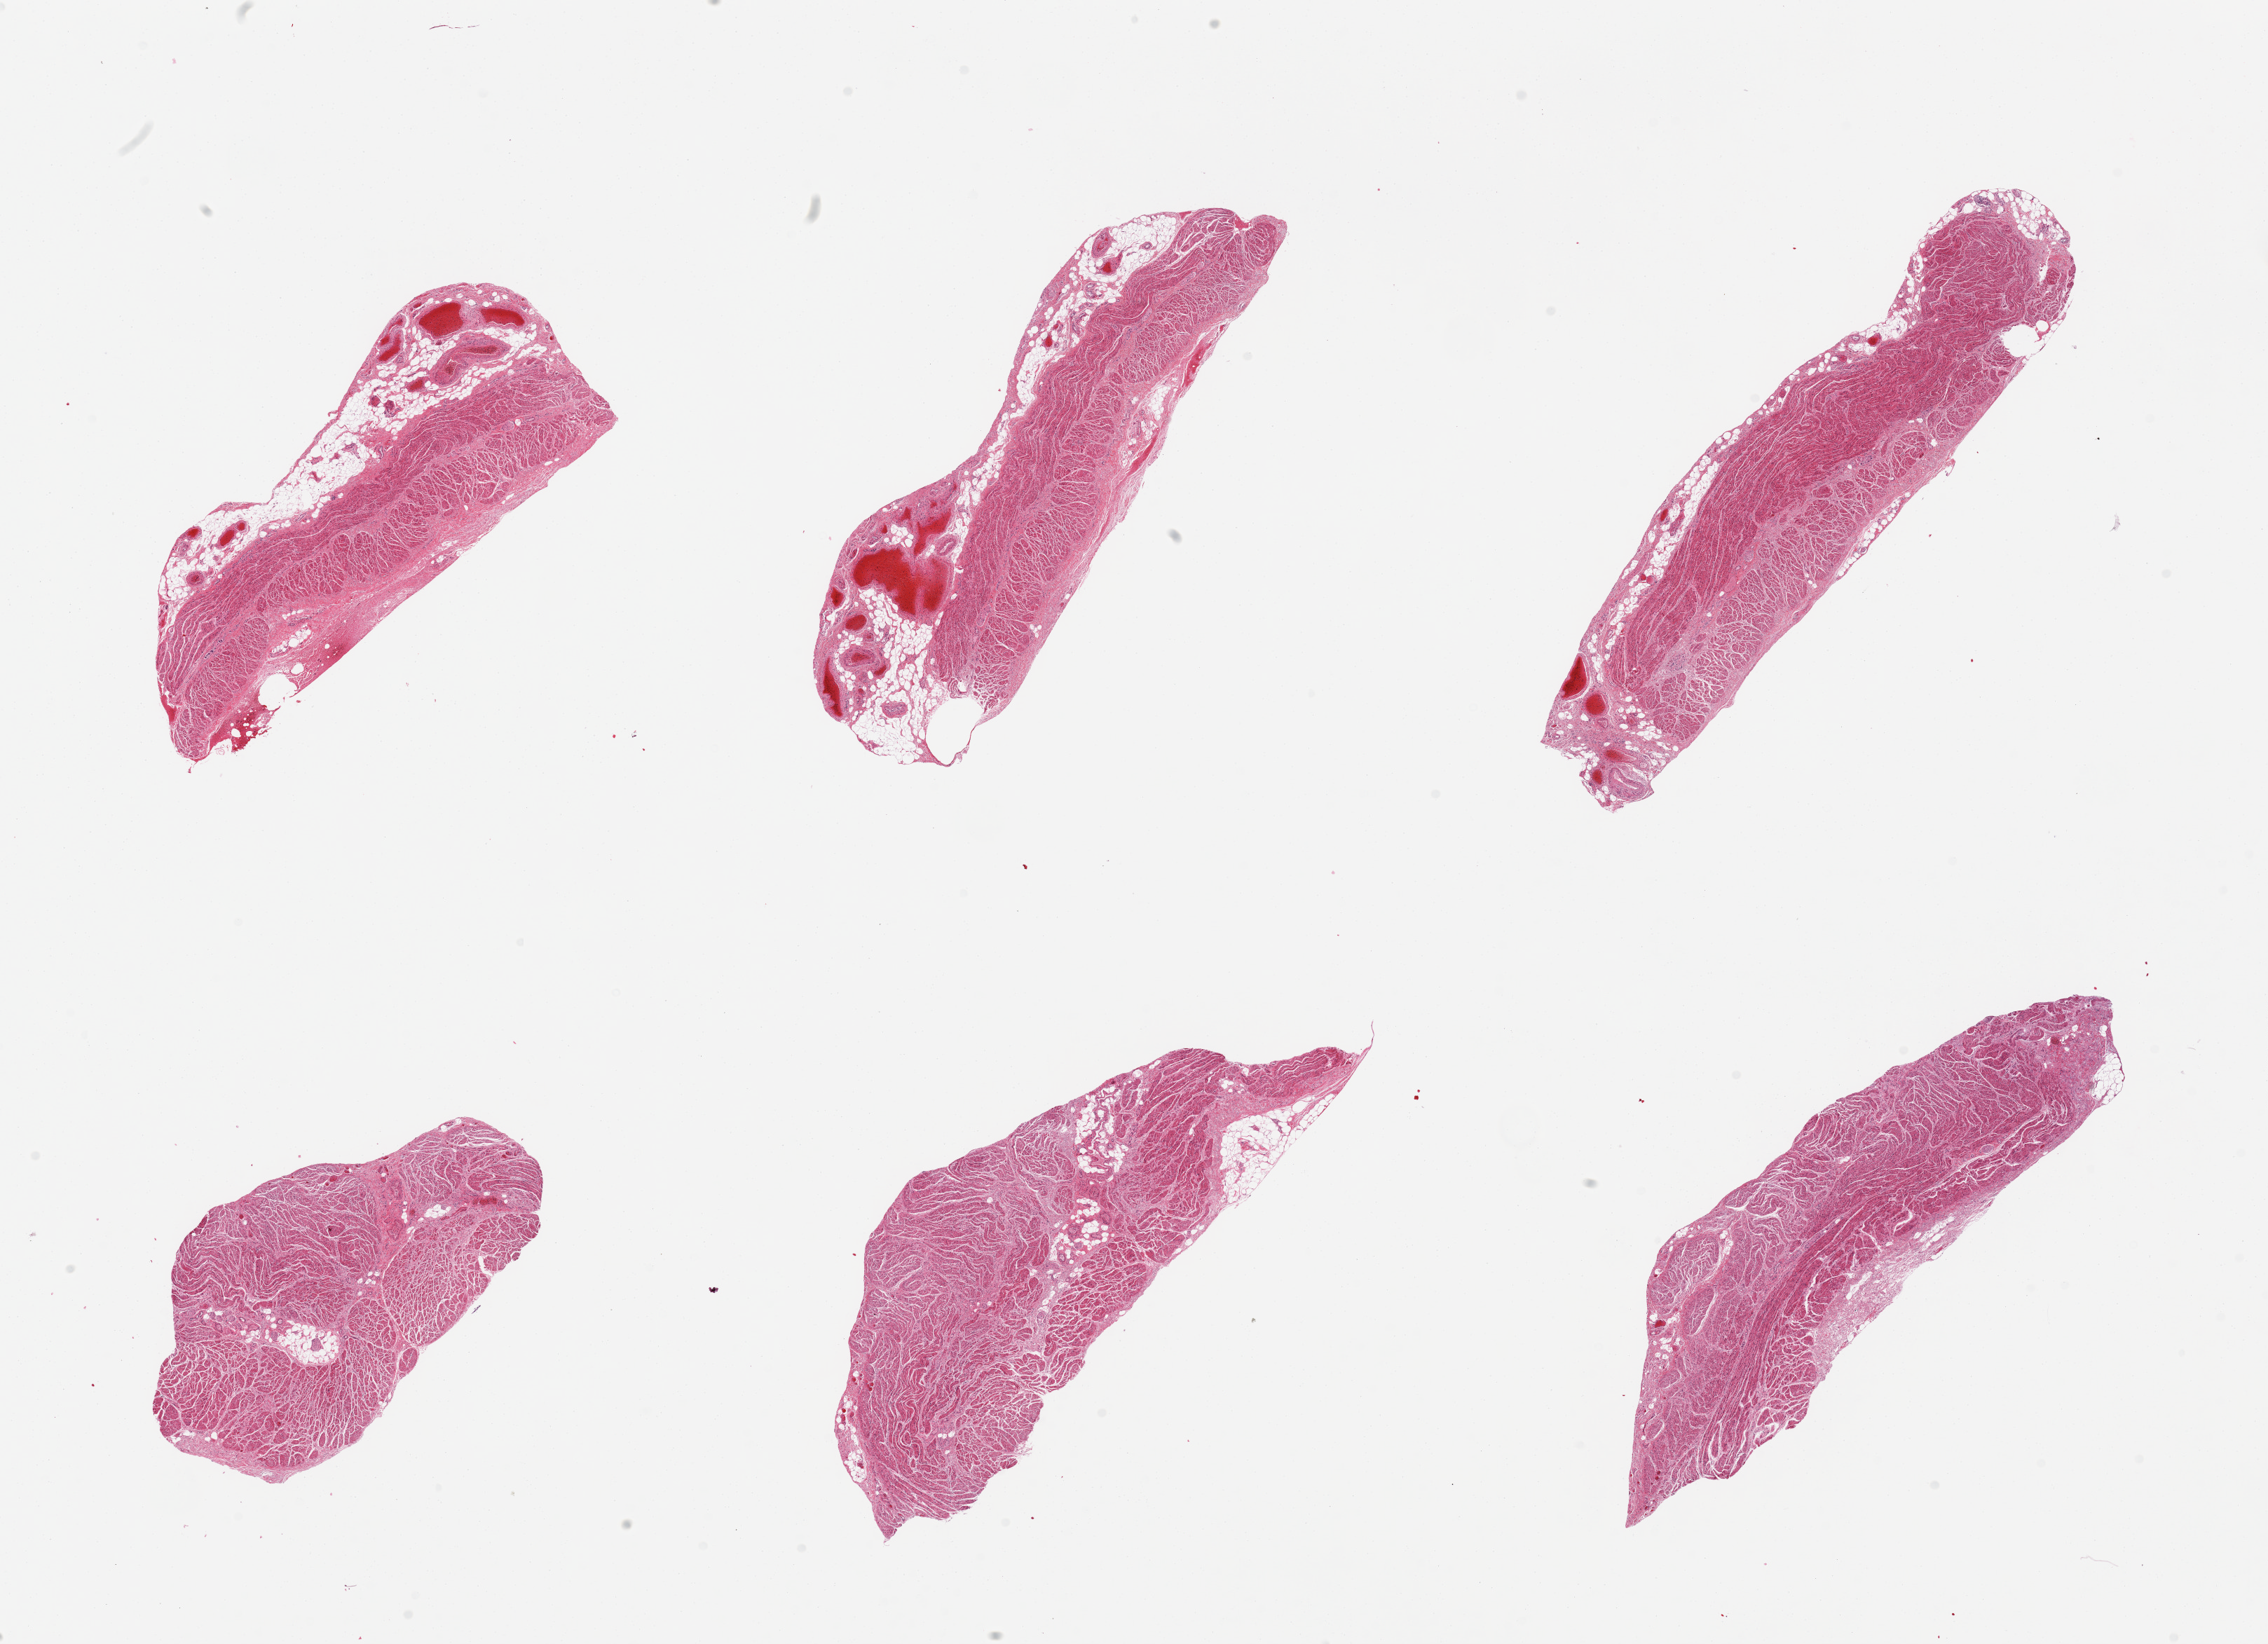
Whole-slide image, hematoxylin and eosin (H&E) stain — a low-resolution overview of the entire scanned area, about 25.6 x 18.6 mm (slide scanned at 20x). PAXgene-fixed, paraffin-embedded tissue. Sampled site (target tissue): gastroesophageal junction. Donor tissue sample. Male donor.
• reviewer comment on this tissue sample: 6 pieces; 3 with up to 1 mm adventitial fat